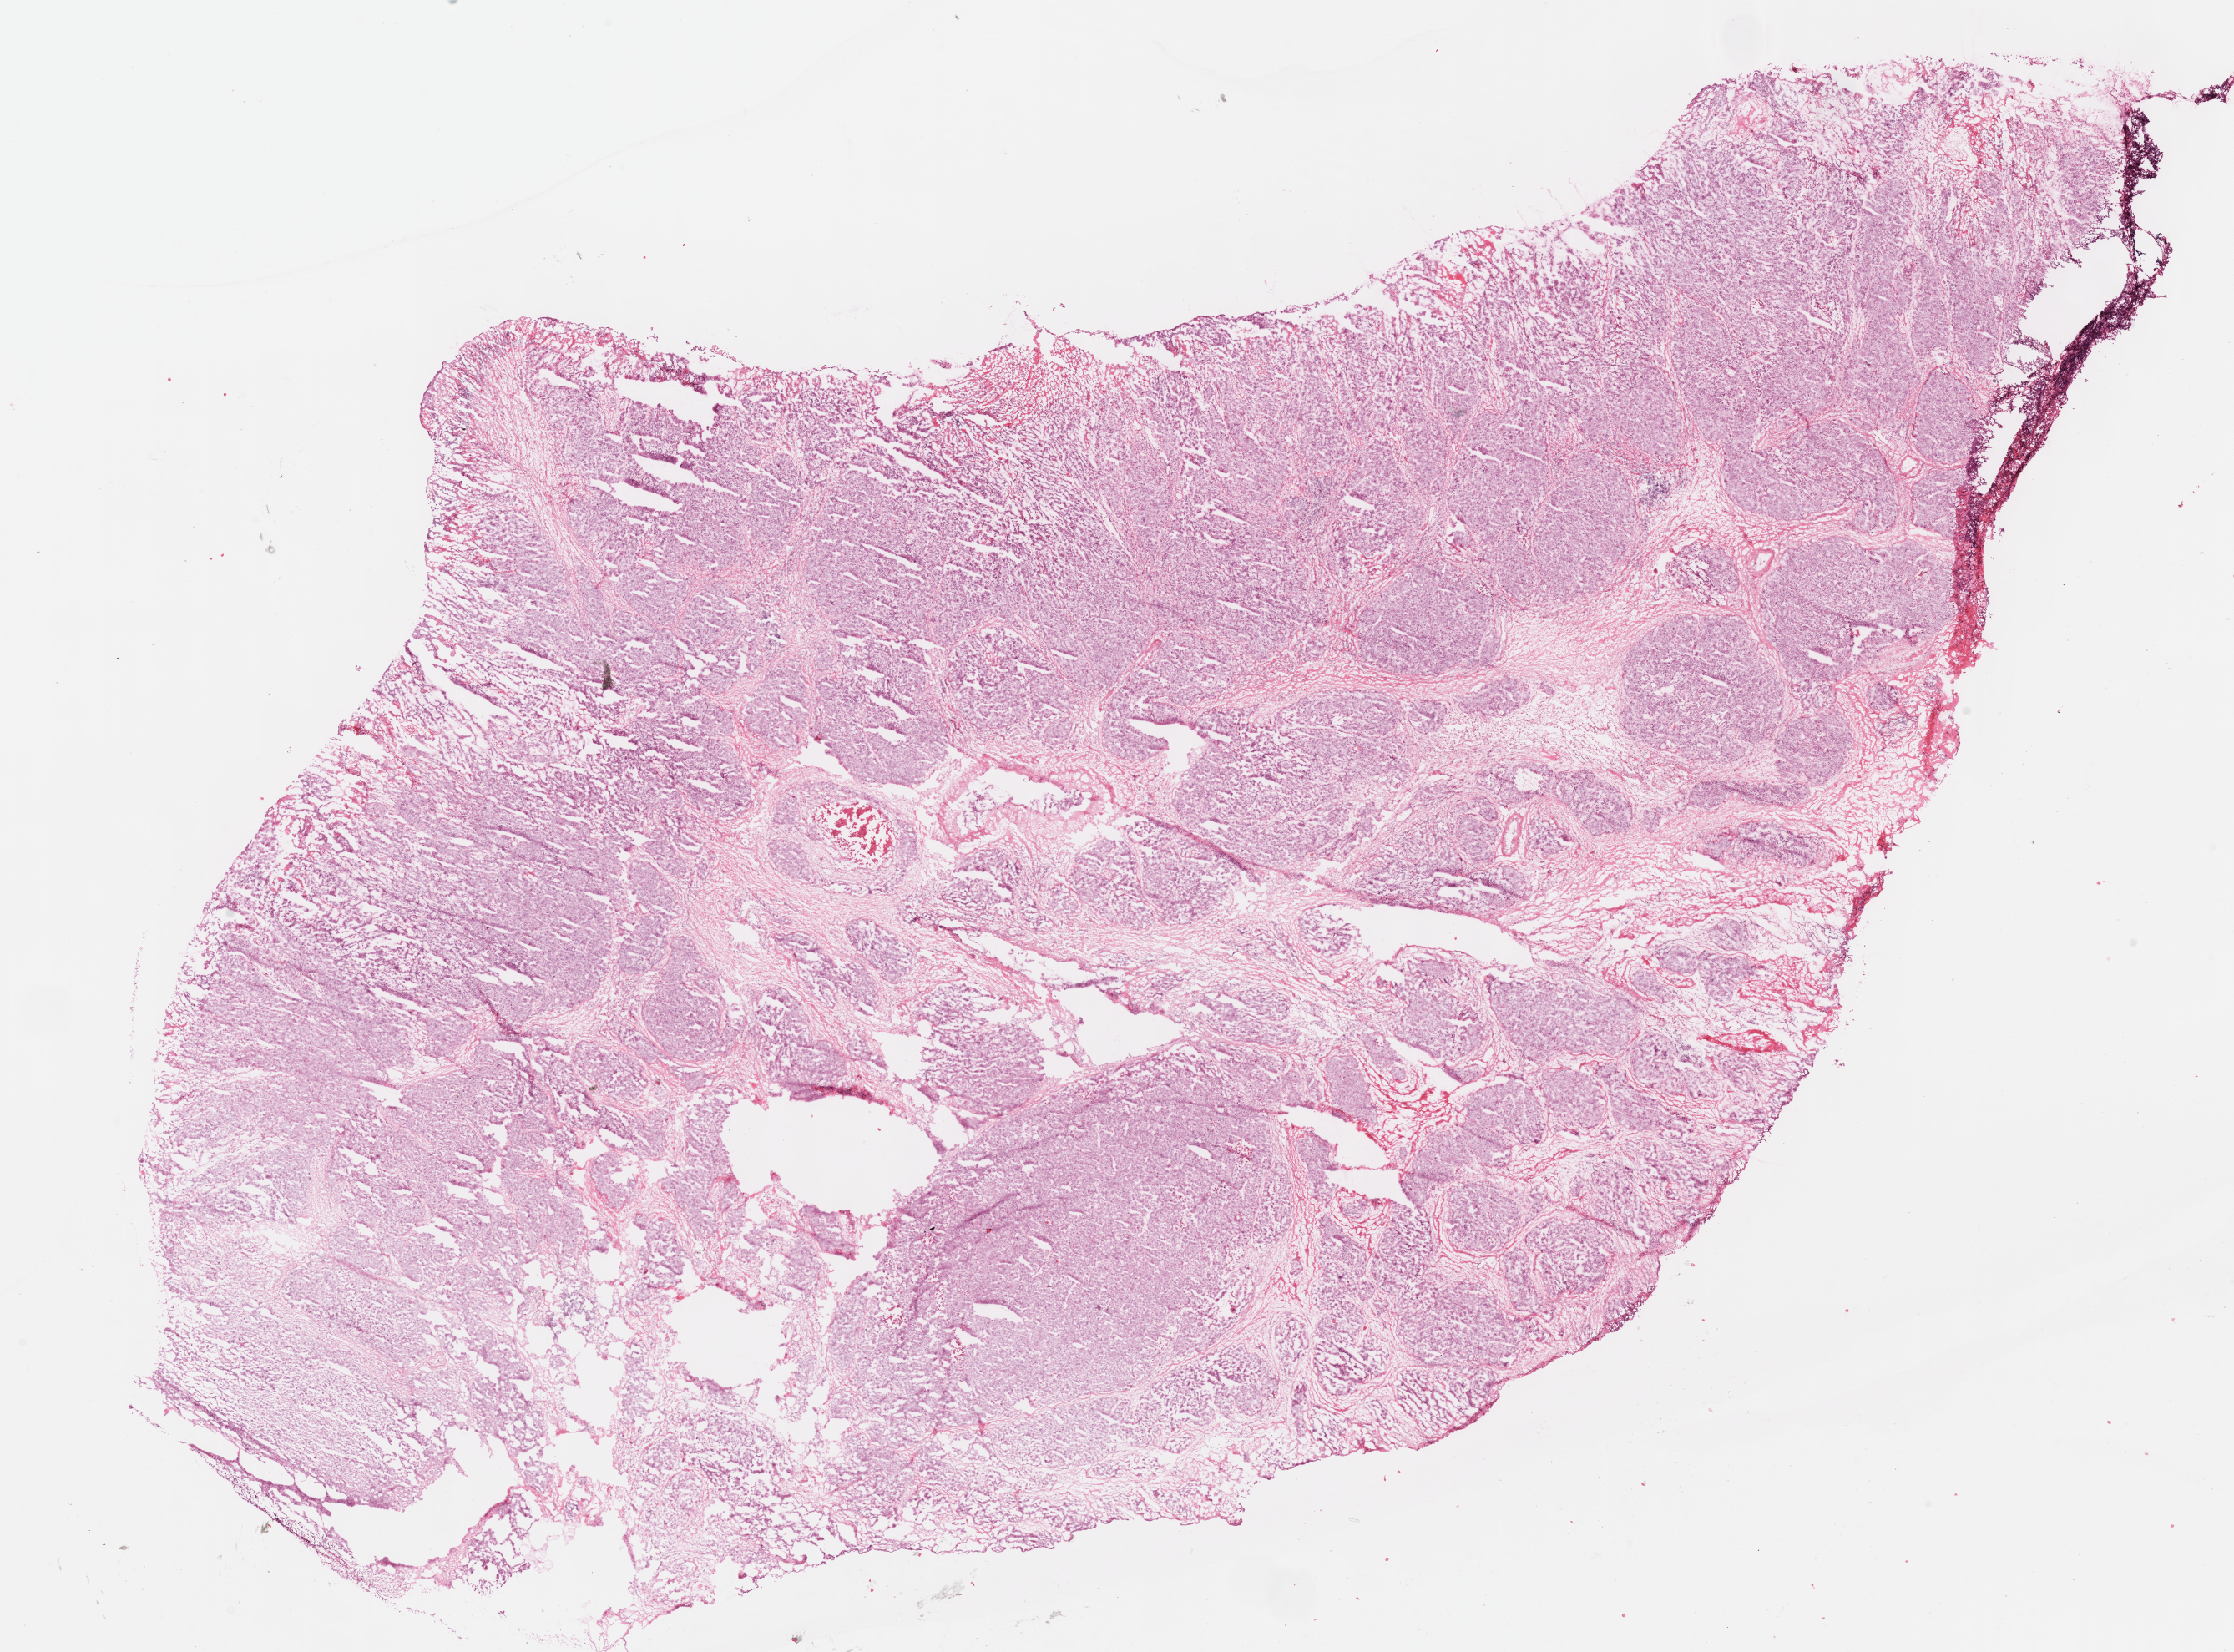
H&E whole-slide image, low-resolution overview of the scanned area, about 21.0 x 15.6 mm; frozen section from the top of the tissue portion; primary tumour sample from the stomach. Female, age 60 years at initial diagnosis. Histologic grade: G3 (poorly differentiated). Slide review estimates, as recorded: tumour cells 85%, tumour nuclei 85%, normal cells 0%, stromal cells 10%, necrosis 5%.
AJCC pathologic stage: IIB. Lymph nodes positive (case pathology): 0 of 5 examined. TNM: T4a N0 M0. Pathologic diagnosis: Adenocarcinoma, intestinal type.